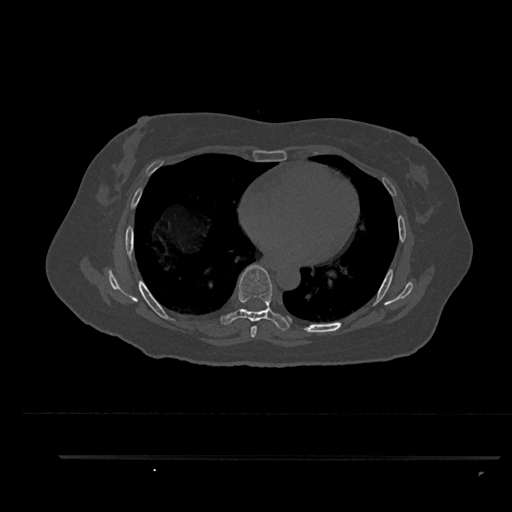
CT including the spine, one axial slice; slice 513 of 797 in the series (ordered by position); 120 kVp; bone window (W 1800 / L 400 HU); 0.5 mm slice thickness; 512 × 512 image matrix, field of view 408 × 408 mm. Female patient, age 44 years. From the clinical record (not read from this slice): primary cancer: renal.
Structures marked on this image (semi-automatic segmentation, software-assisted and operator-edited):
- T6 vertebra: box from (x=251, y=326) to (x=257, y=338) px
- T7 vertebra: (x=220, y=265)–(x=291, y=331)